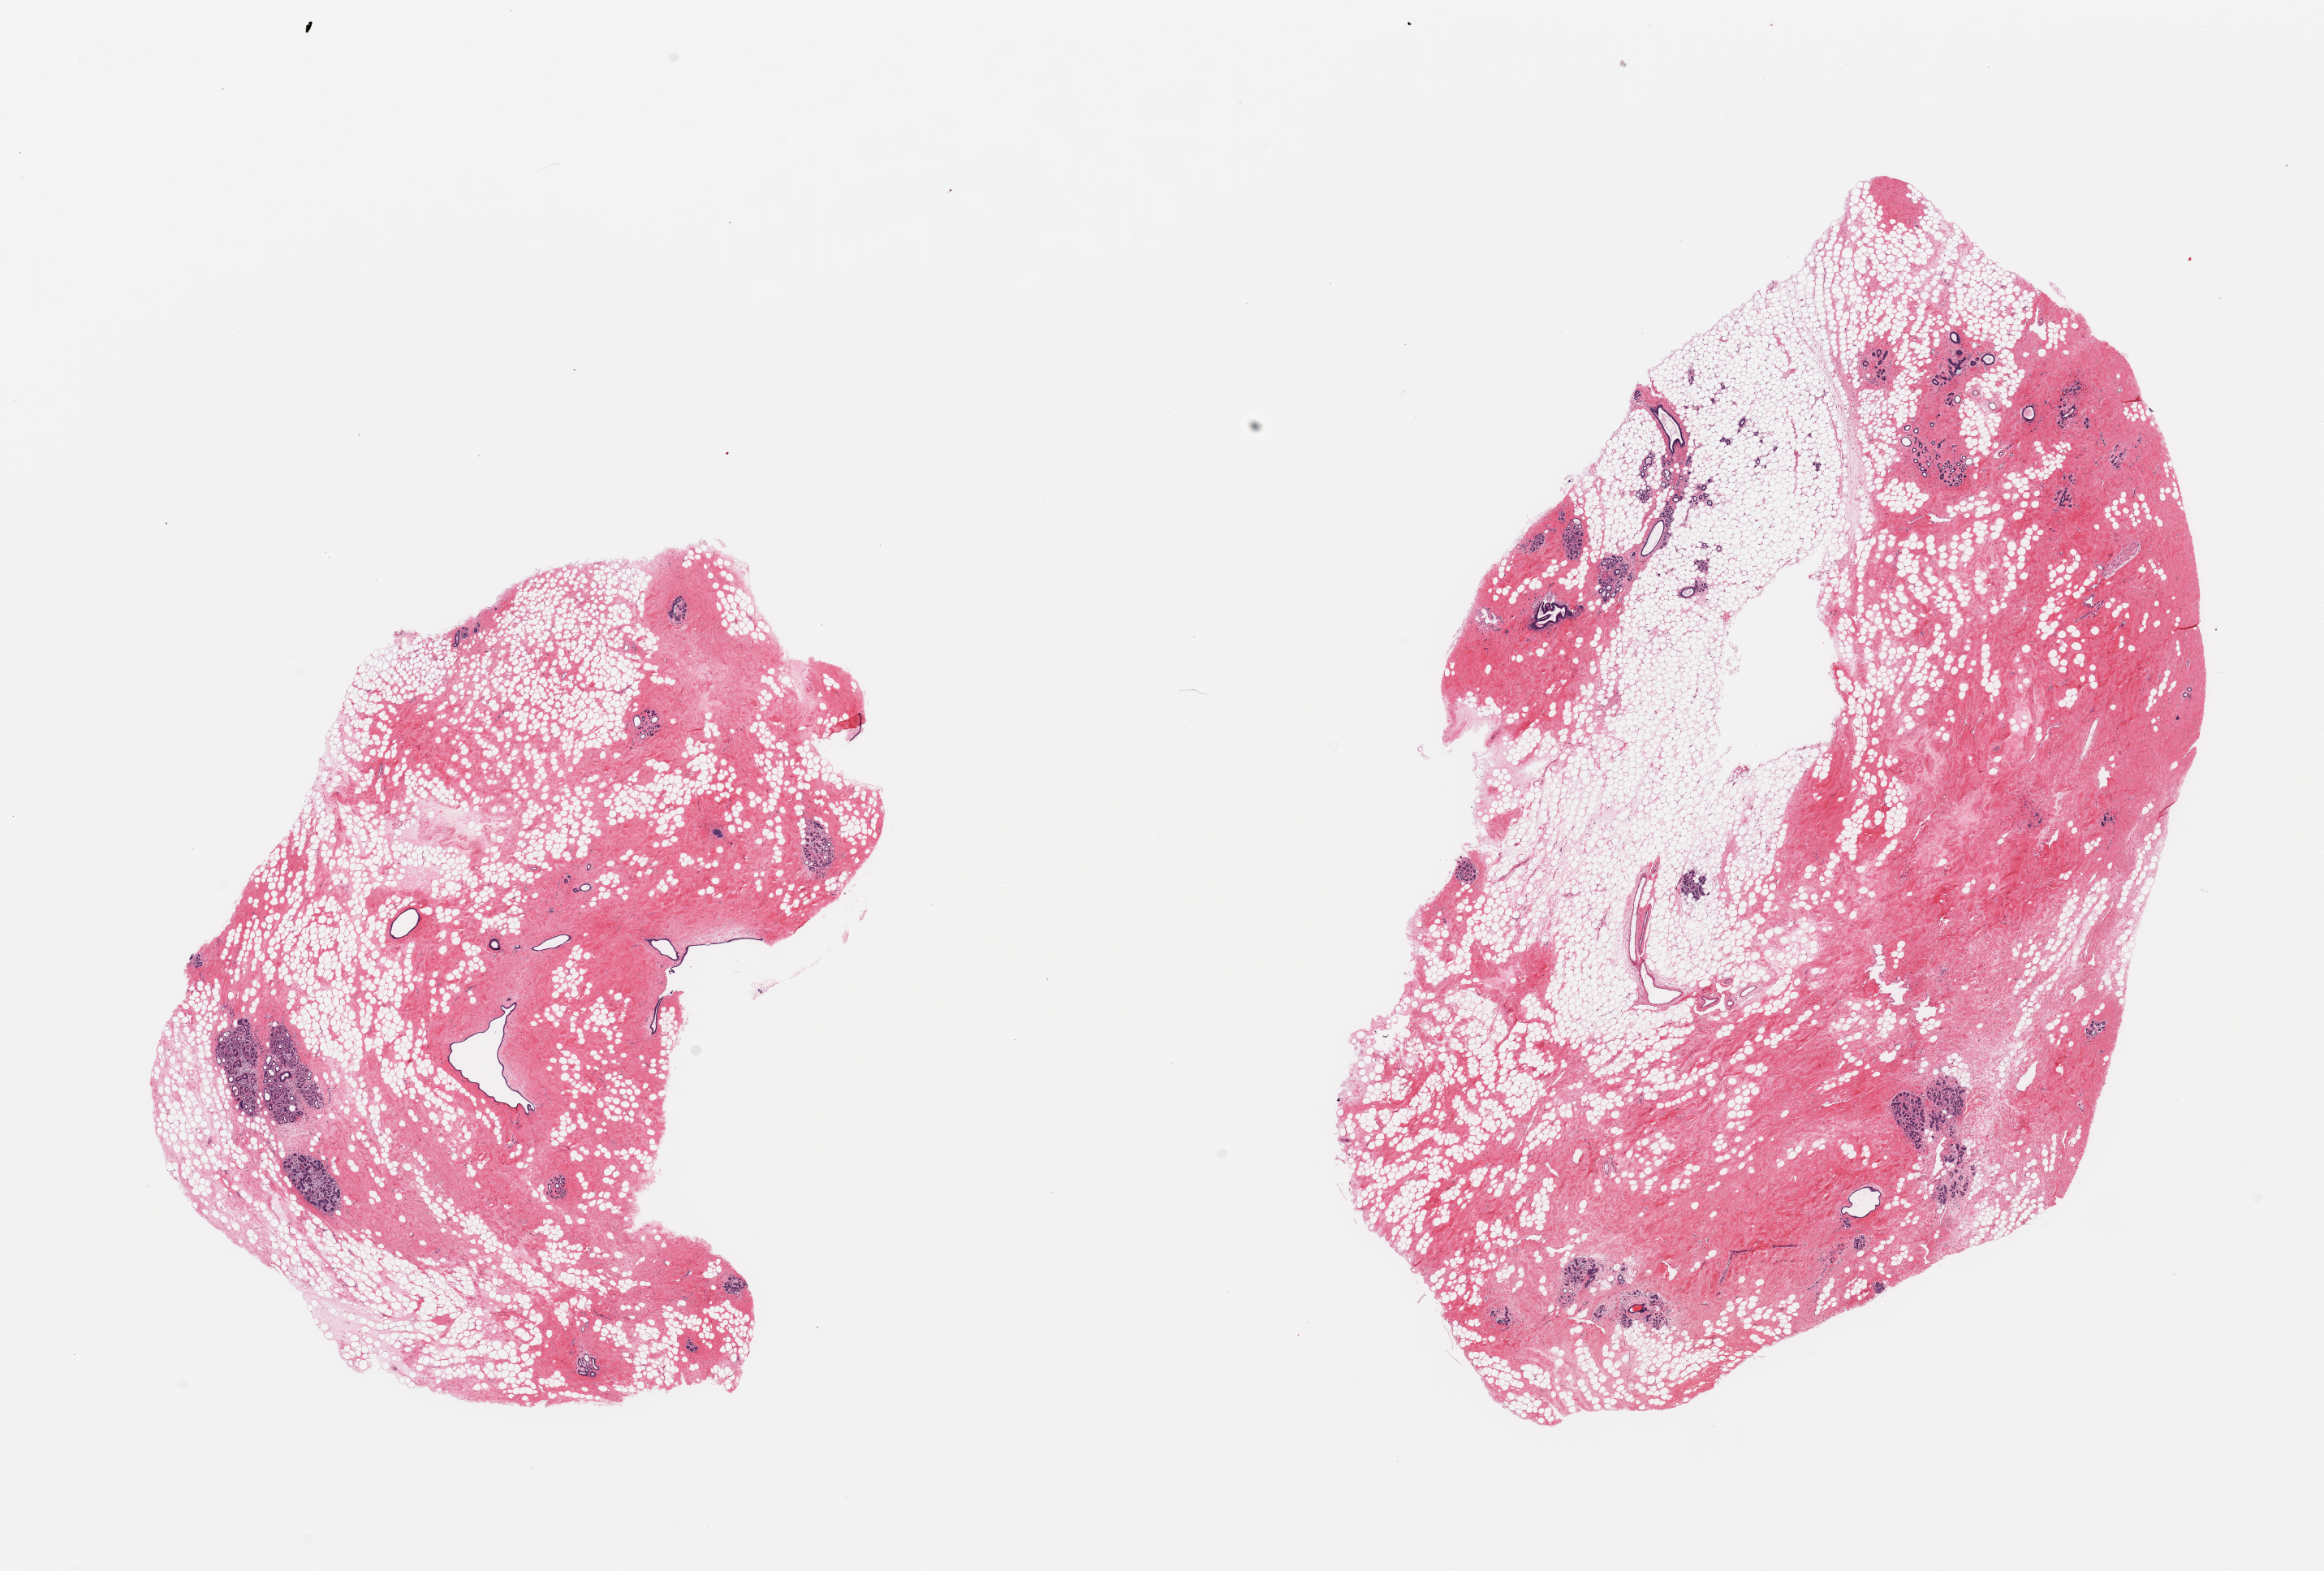
Whole-slide image, hematoxylin and eosin (H&E) stain, brightfield, low-resolution overview of the scanned area, about 22.6 x 15.3 mm, PAXgene-fixed, paraffin-embedded tissue, sampled site (target tissue): breast, tissue donor sample. Female donor.
- reviewer comment on this tissue sample: 2 pieces, fibrocystic changes; lobular/ductal elements present